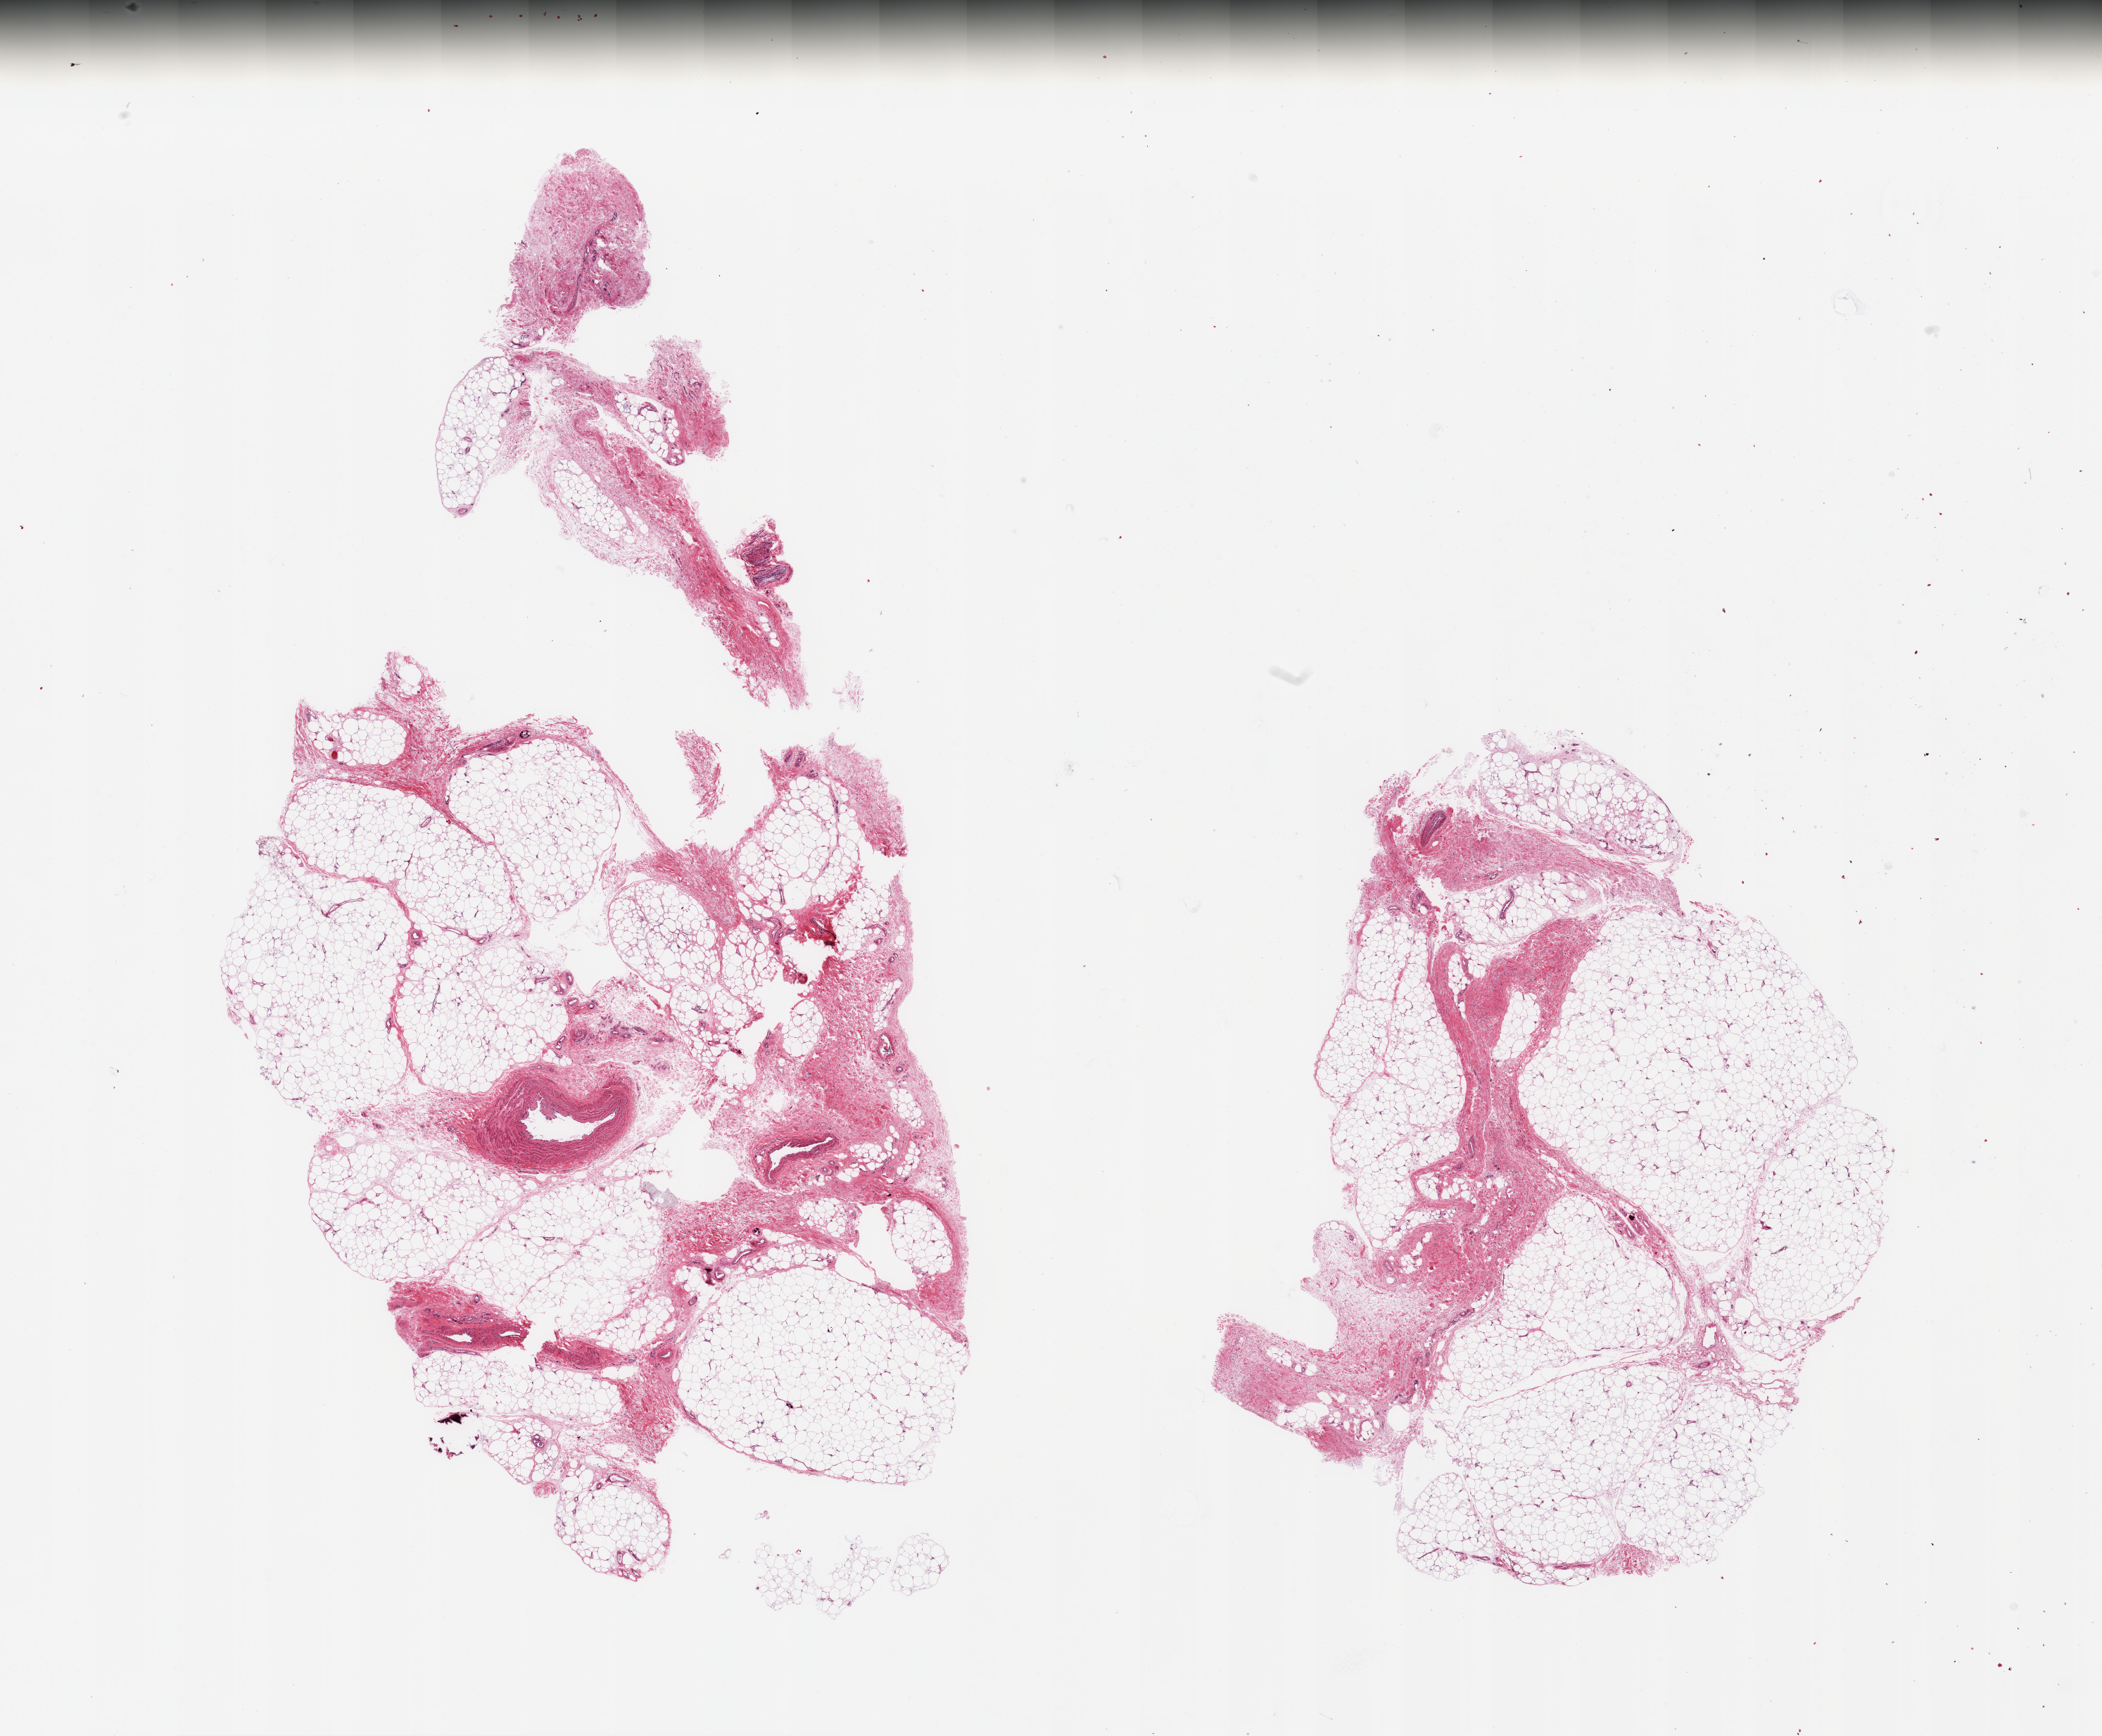
Digitized hematoxylin and eosin (H&E)-stained section, brightfield, low-resolution overview of the scanned area, about 23.6 x 19.5 mm (from a 20x scan), PAXgene-fixed, paraffin-embedded tissue, section of adipose tissue (target tissue), tissue donor sample.
Review note (as recorded): 2 pieces; adipose with 20% fibrovascular content.